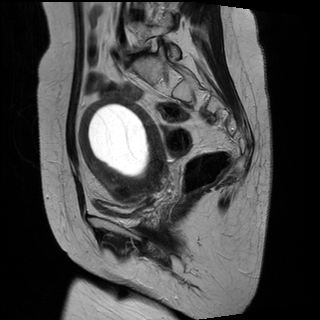
Pelvic MRI for cervical cancer, one sagittal slice; position 19 of 29 along the scan axis; T2-weighted; 1.5 T; TE 89 ms, TR 2930 ms; 4 mm slice thickness; 320 × 320 image matrix. Patient: female, 49 years.
Structures marked on this image (manually delineated by an expert):
- uterus and cervix: bounding box [x1, y1, x2, y2] px = [78, 98, 167, 203]